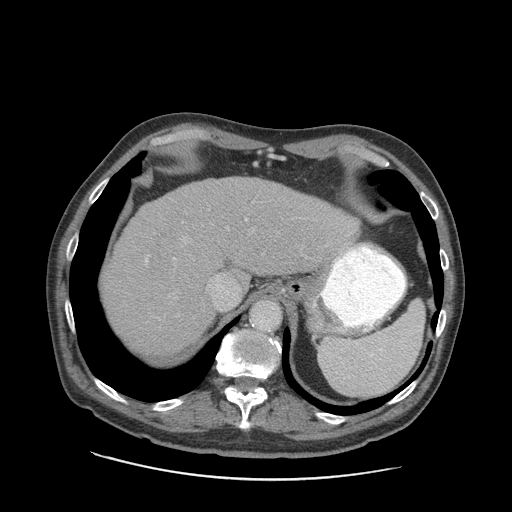
Contrast-enhanced abdominal CT (liver protocol), one axial slice; slice 69 of 89 in the series (ordered by position); 140 kVp; soft-tissue window (W 400 / L 40 HU); 2.5 mm slice thickness; 512 × 512 image matrix, field of view 420 × 420 mm. From the clinical record (not read from this slice): diagnosis: hepatocellular carcinoma (patient treated with transarterial chemoembolisation; whether this scan precedes or follows treatment is not stated here); TNM stage (as recorded): Stage-I; Child-Pugh class: A.
Annotated regions visible in this slice (semi-automatically segmented with operator editing):
- abdominal aorta: bounding box <252,300,279,329> (left, top, right, bottom; pixels)
- liver parenchyma outside the tumour (the mass and vessels are separate outlines, so this box may not span the whole liver): <104,176,358,356>
- liver vessels: <145,201,352,320>